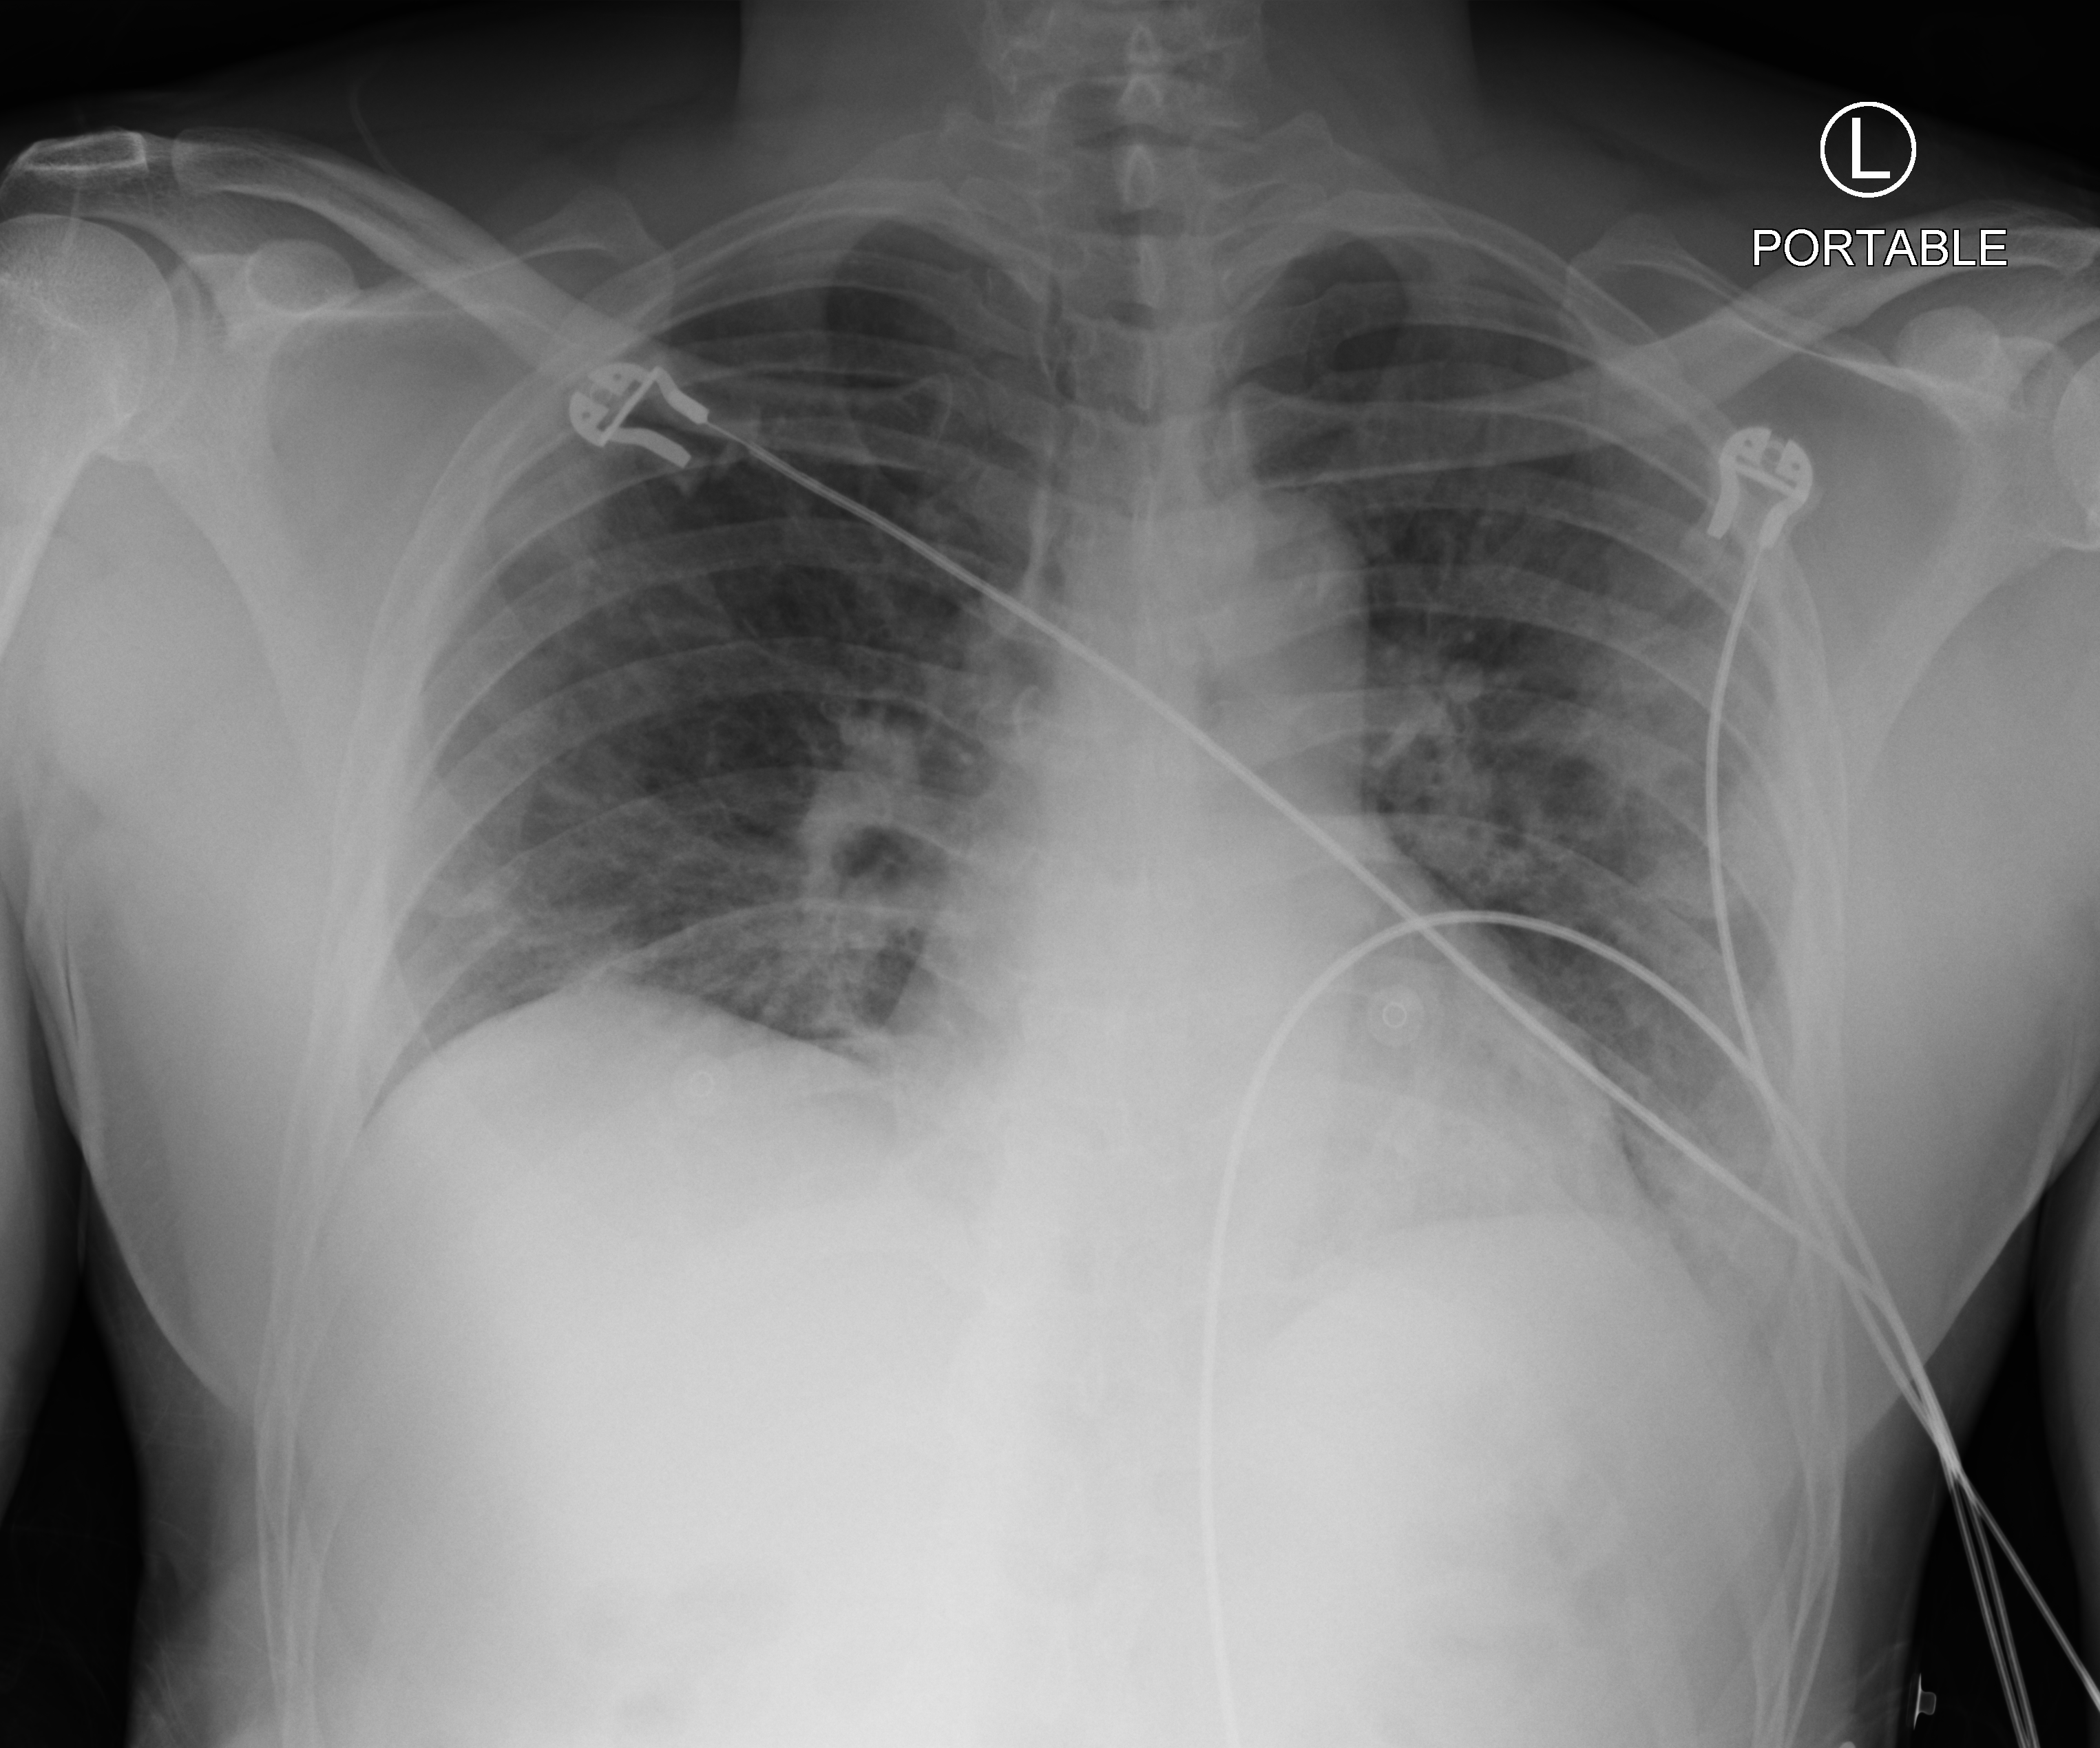
Bedside chest radiograph (computed radiography); anteroposterior (AP) projection. Patient hospitalised with COVID-19; male, aged 18–59 years.
Admission-level facts for this patient (not findings on this image; timing relative to this image not recorded): admitted to intensive care during this hospital stay: no.